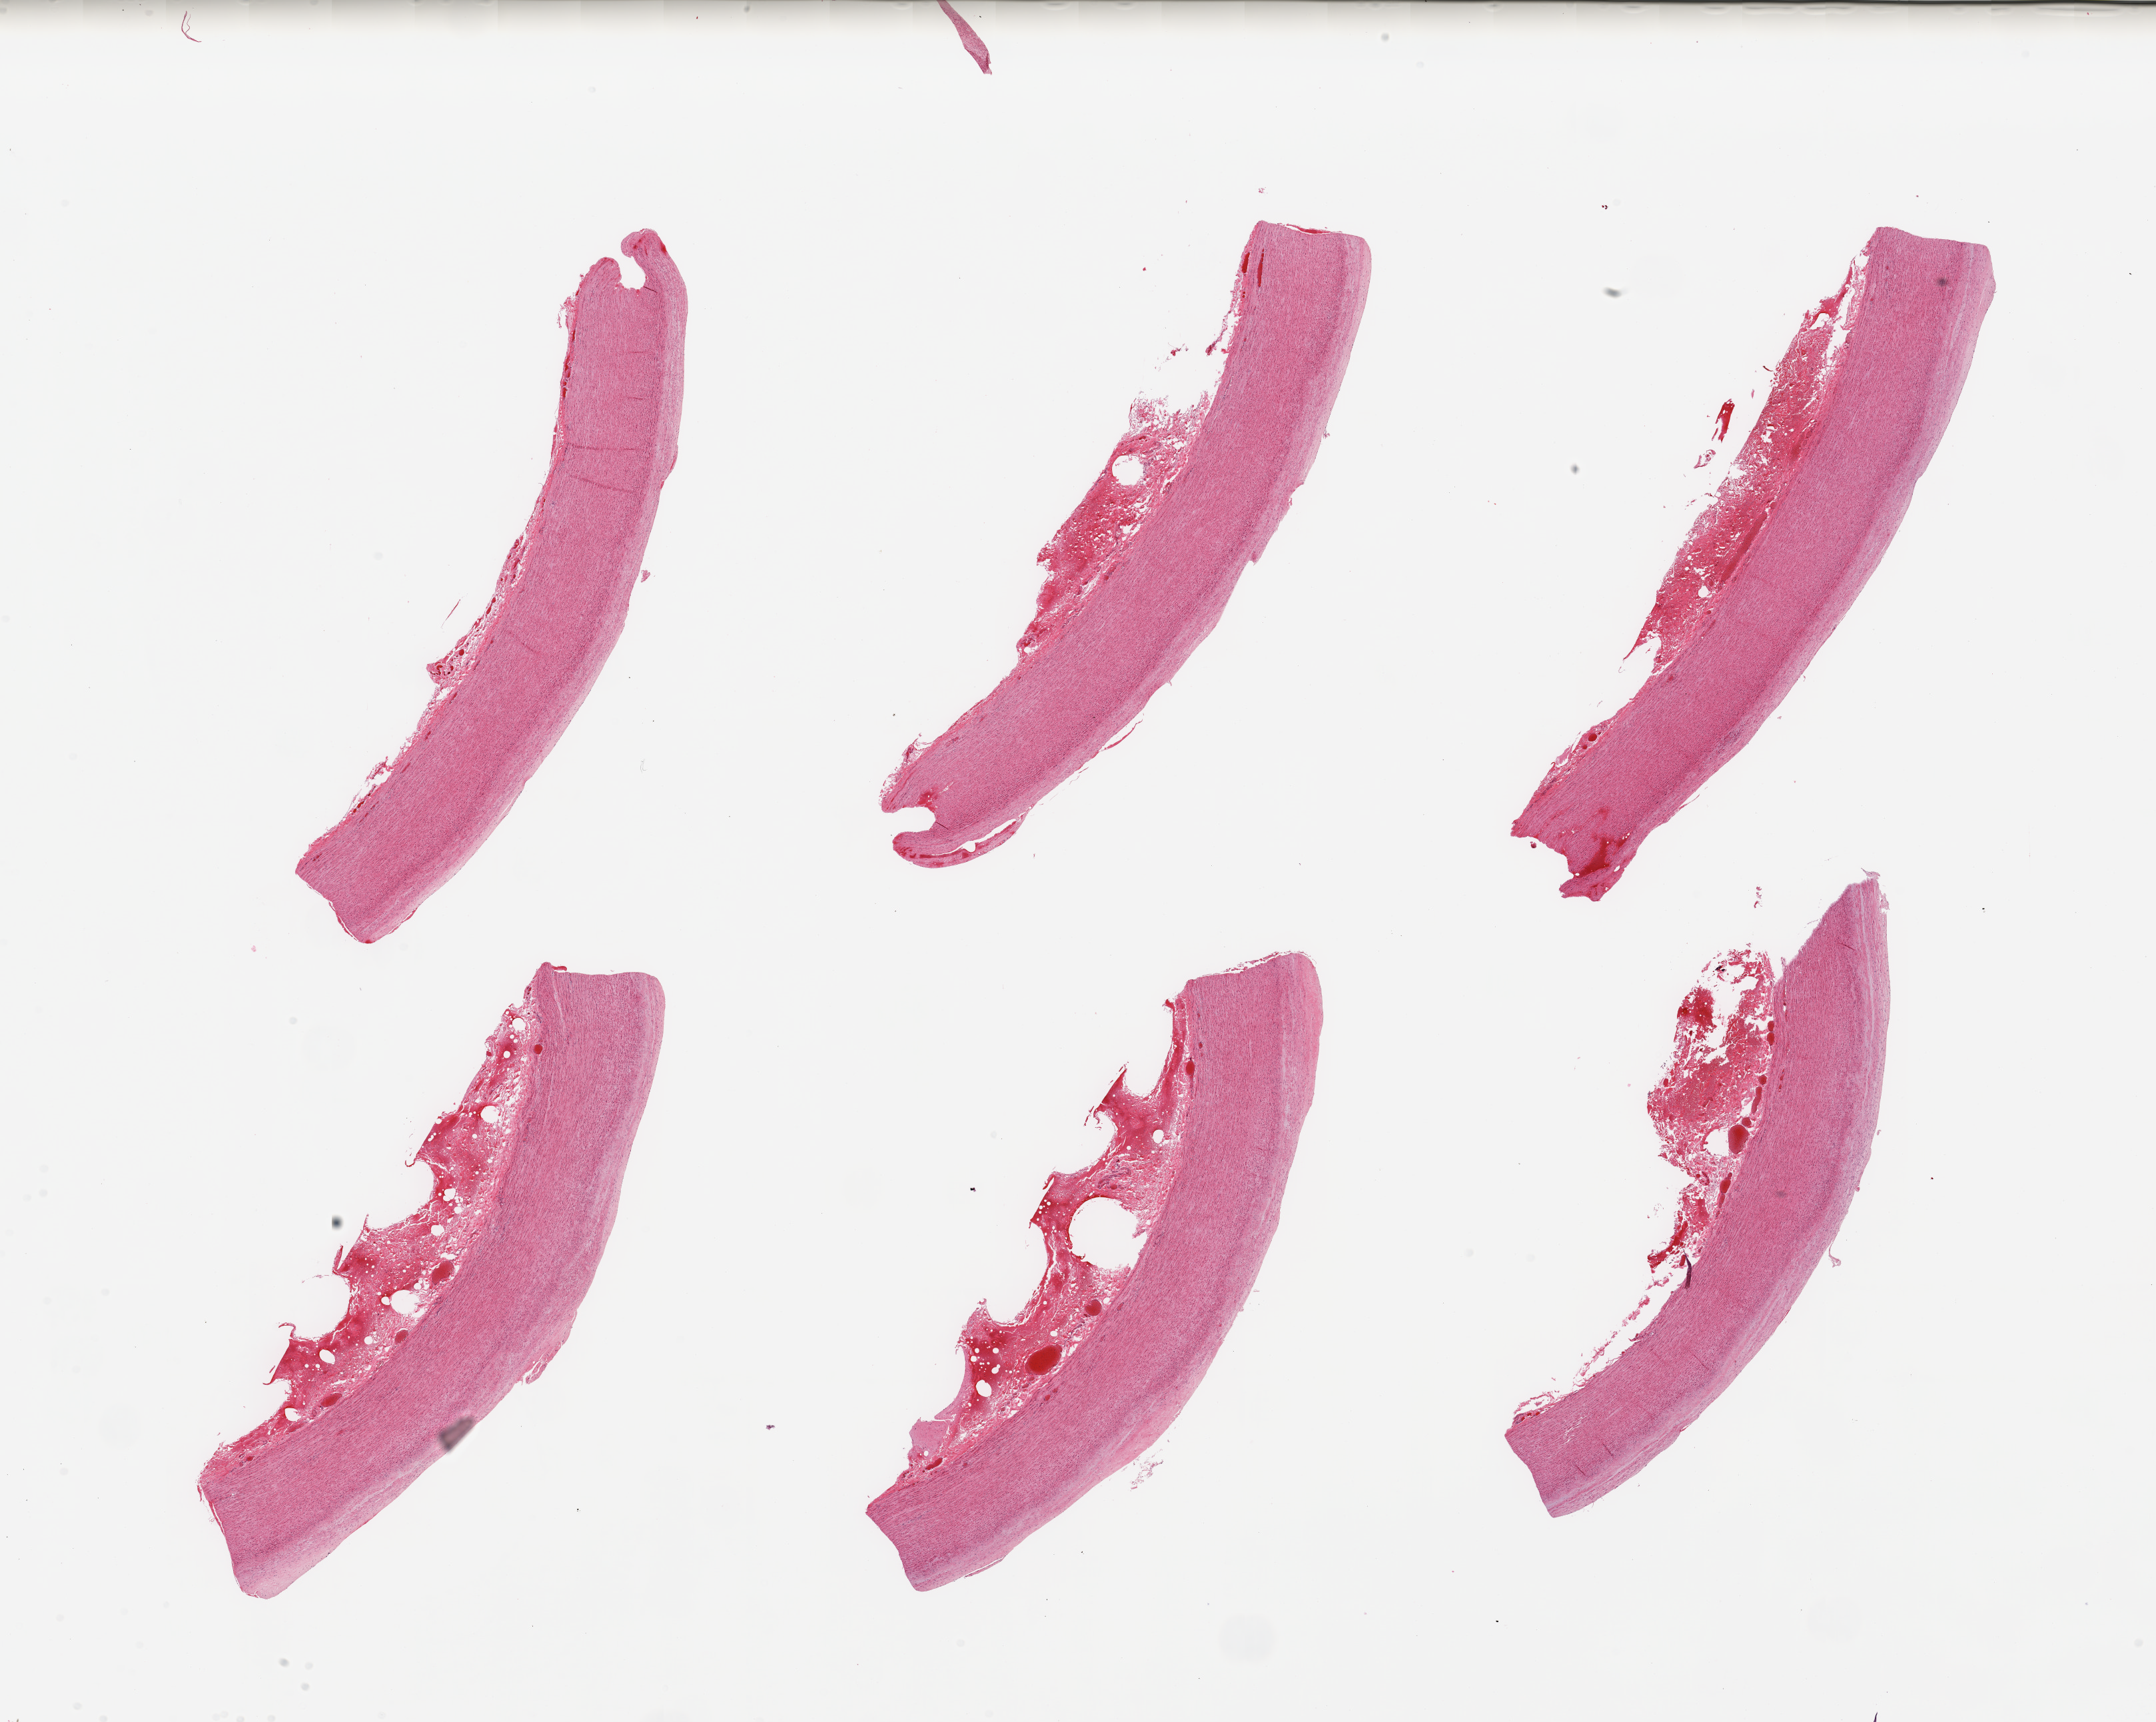
Whole-slide image, hematoxylin and eosin (H&E) stain, brightfield, whole scanned area (about 25.6 x 20.4 mm, from a 20x scan) shown as a low-resolution overview, PAXgene-fixed, paraffin-embedded tissue, section of aorta (target tissue), tissue donor sample. Donor sex: male.
Reviewer comment on this tissue sample: 6 pieces; atherosclerosis.